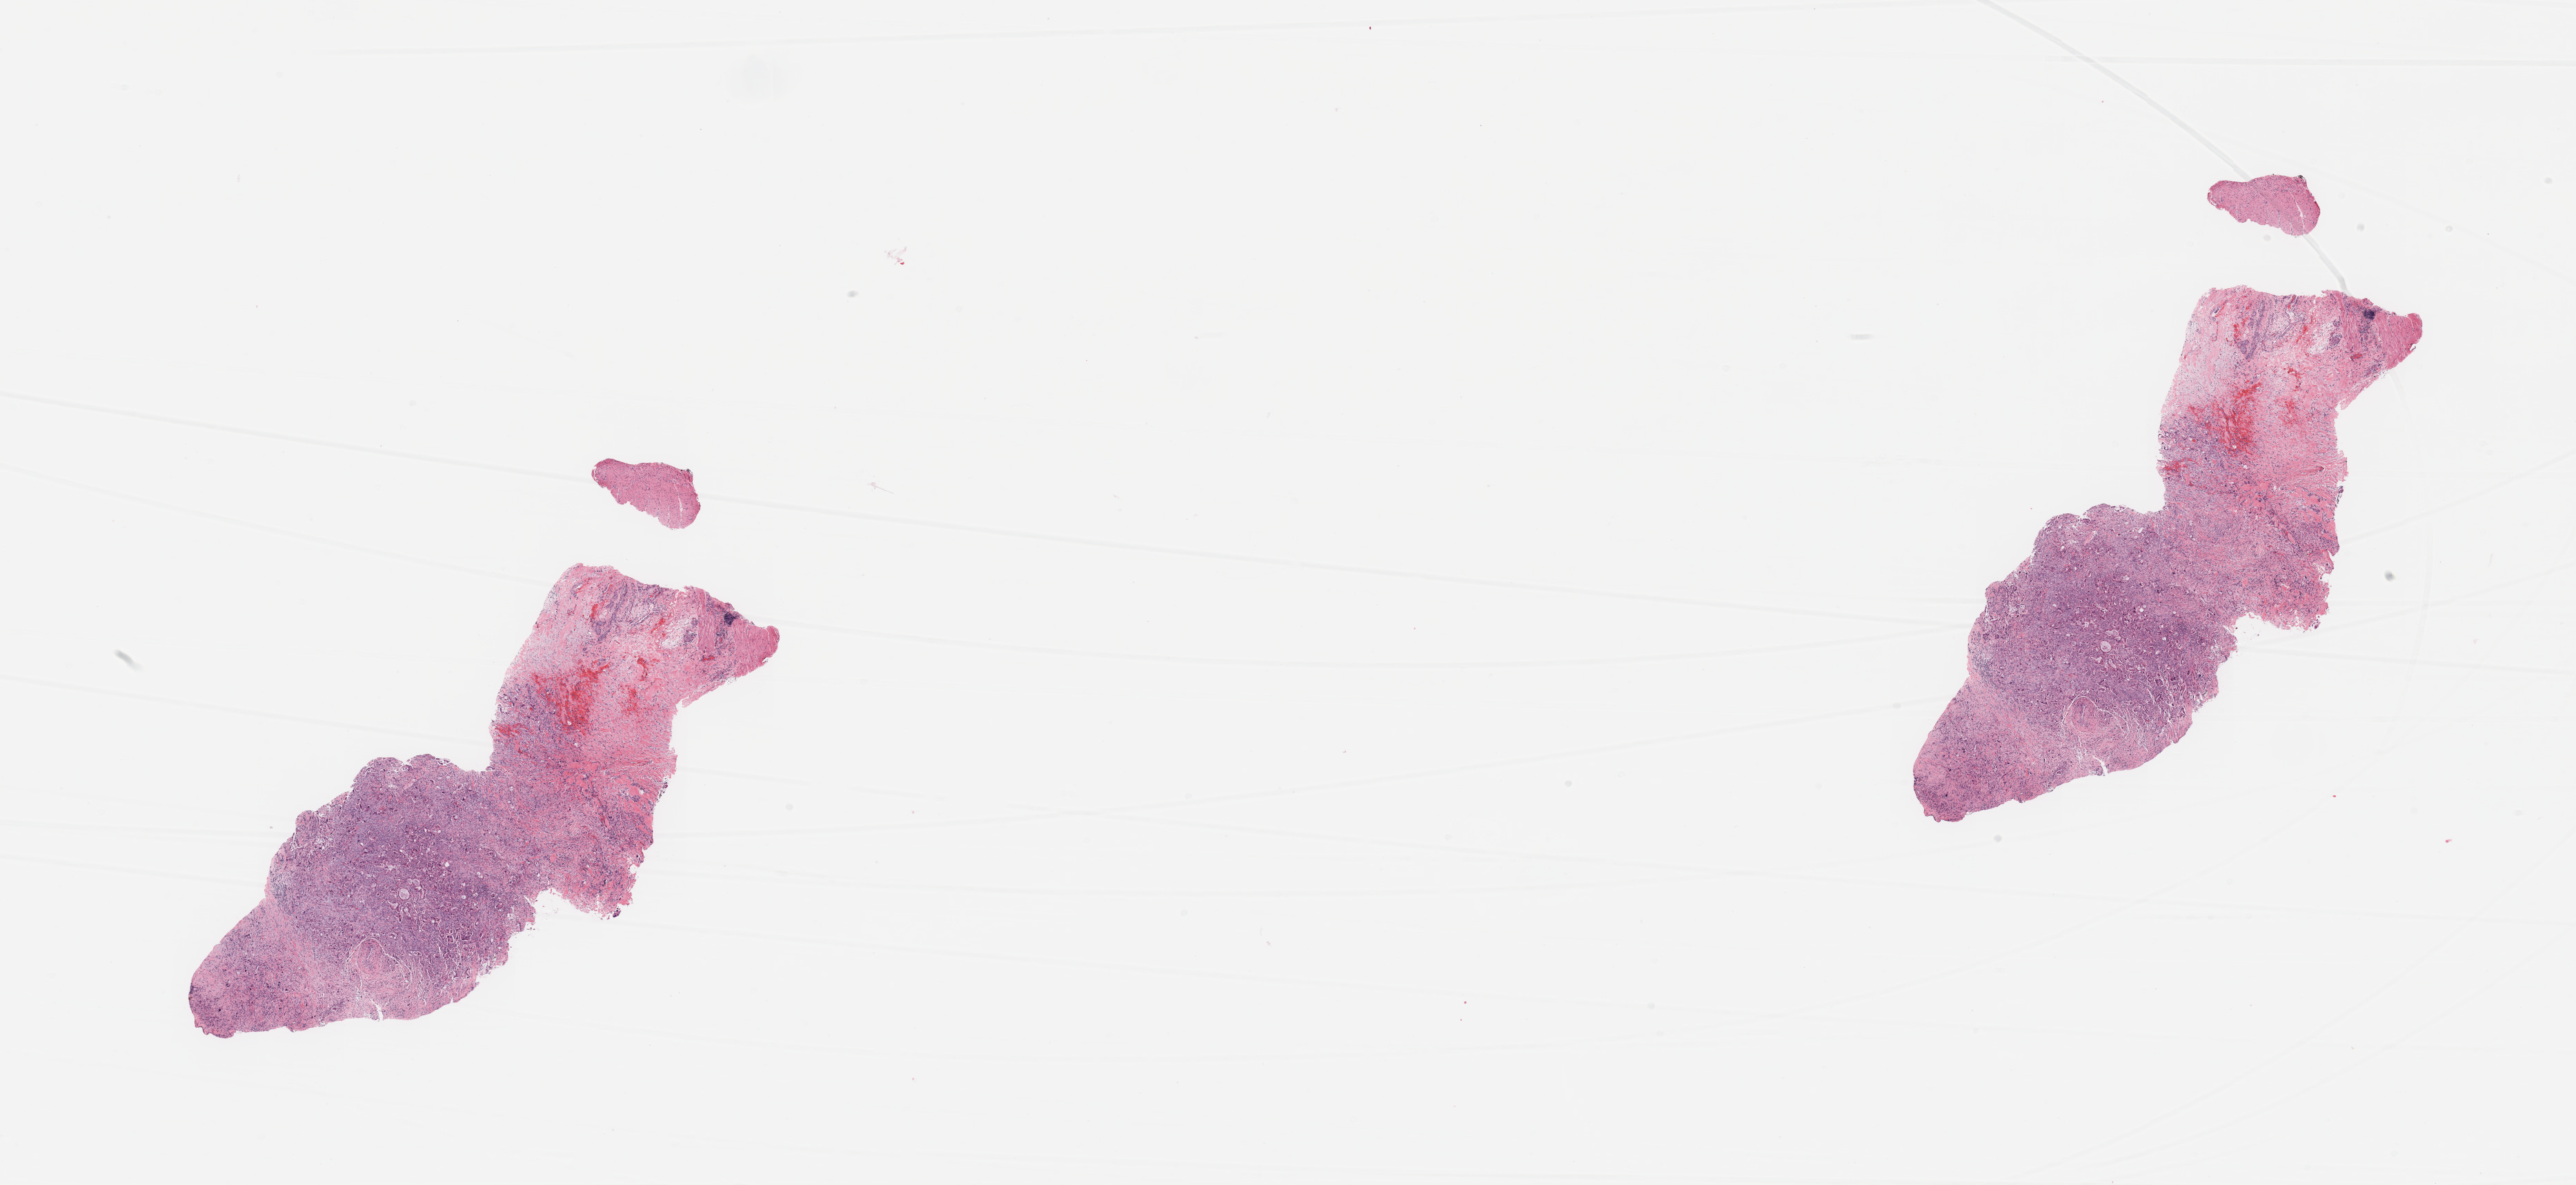
Hematoxylin and eosin (H&E) stained whole-slide image — shown as a low-resolution overview of the whole scanned area (about 29.5 x 13.6 mm, slide scanned at 20x); tumour tissue sample, sampled site: pancreas. Patient: male, age 66 years. Histologic grade: G3 (poorly differentiated). Pathologist review of this section (percent, as recorded): tumour nuclei 30%, necrosis 0%.
AJCC pathologic stage: IIB. Primary tumour site (as recorded): head. Histologic diagnosis: Infiltrating duct carcinoma, NOS.